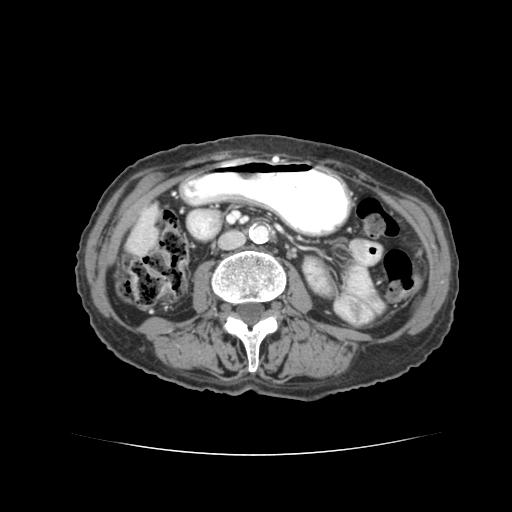
Contrast-enhanced abdominal CT (liver protocol), one axial slice; slice 8 of 77 in the series (ordered by position); reconstruction kernel STANDARD; 120 kVp; soft-tissue window (W 400 / L 40 HU); 2.5 mm slice thickness; 512 × 512 image matrix. From the clinical record (not read from this slice): diagnosis: hepatocellular carcinoma (patient treated with transarterial chemoembolisation; whether this scan precedes or follows treatment is not stated here); TNM stage (as recorded): Stage-I.
Outlined on this slice (semi-automatically segmented with operator editing):
- liver parenchyma outside the tumour (the mass and vessels are separate outlines, so this box may not span the whole liver): box from (x=134, y=214) to (x=148, y=231) px